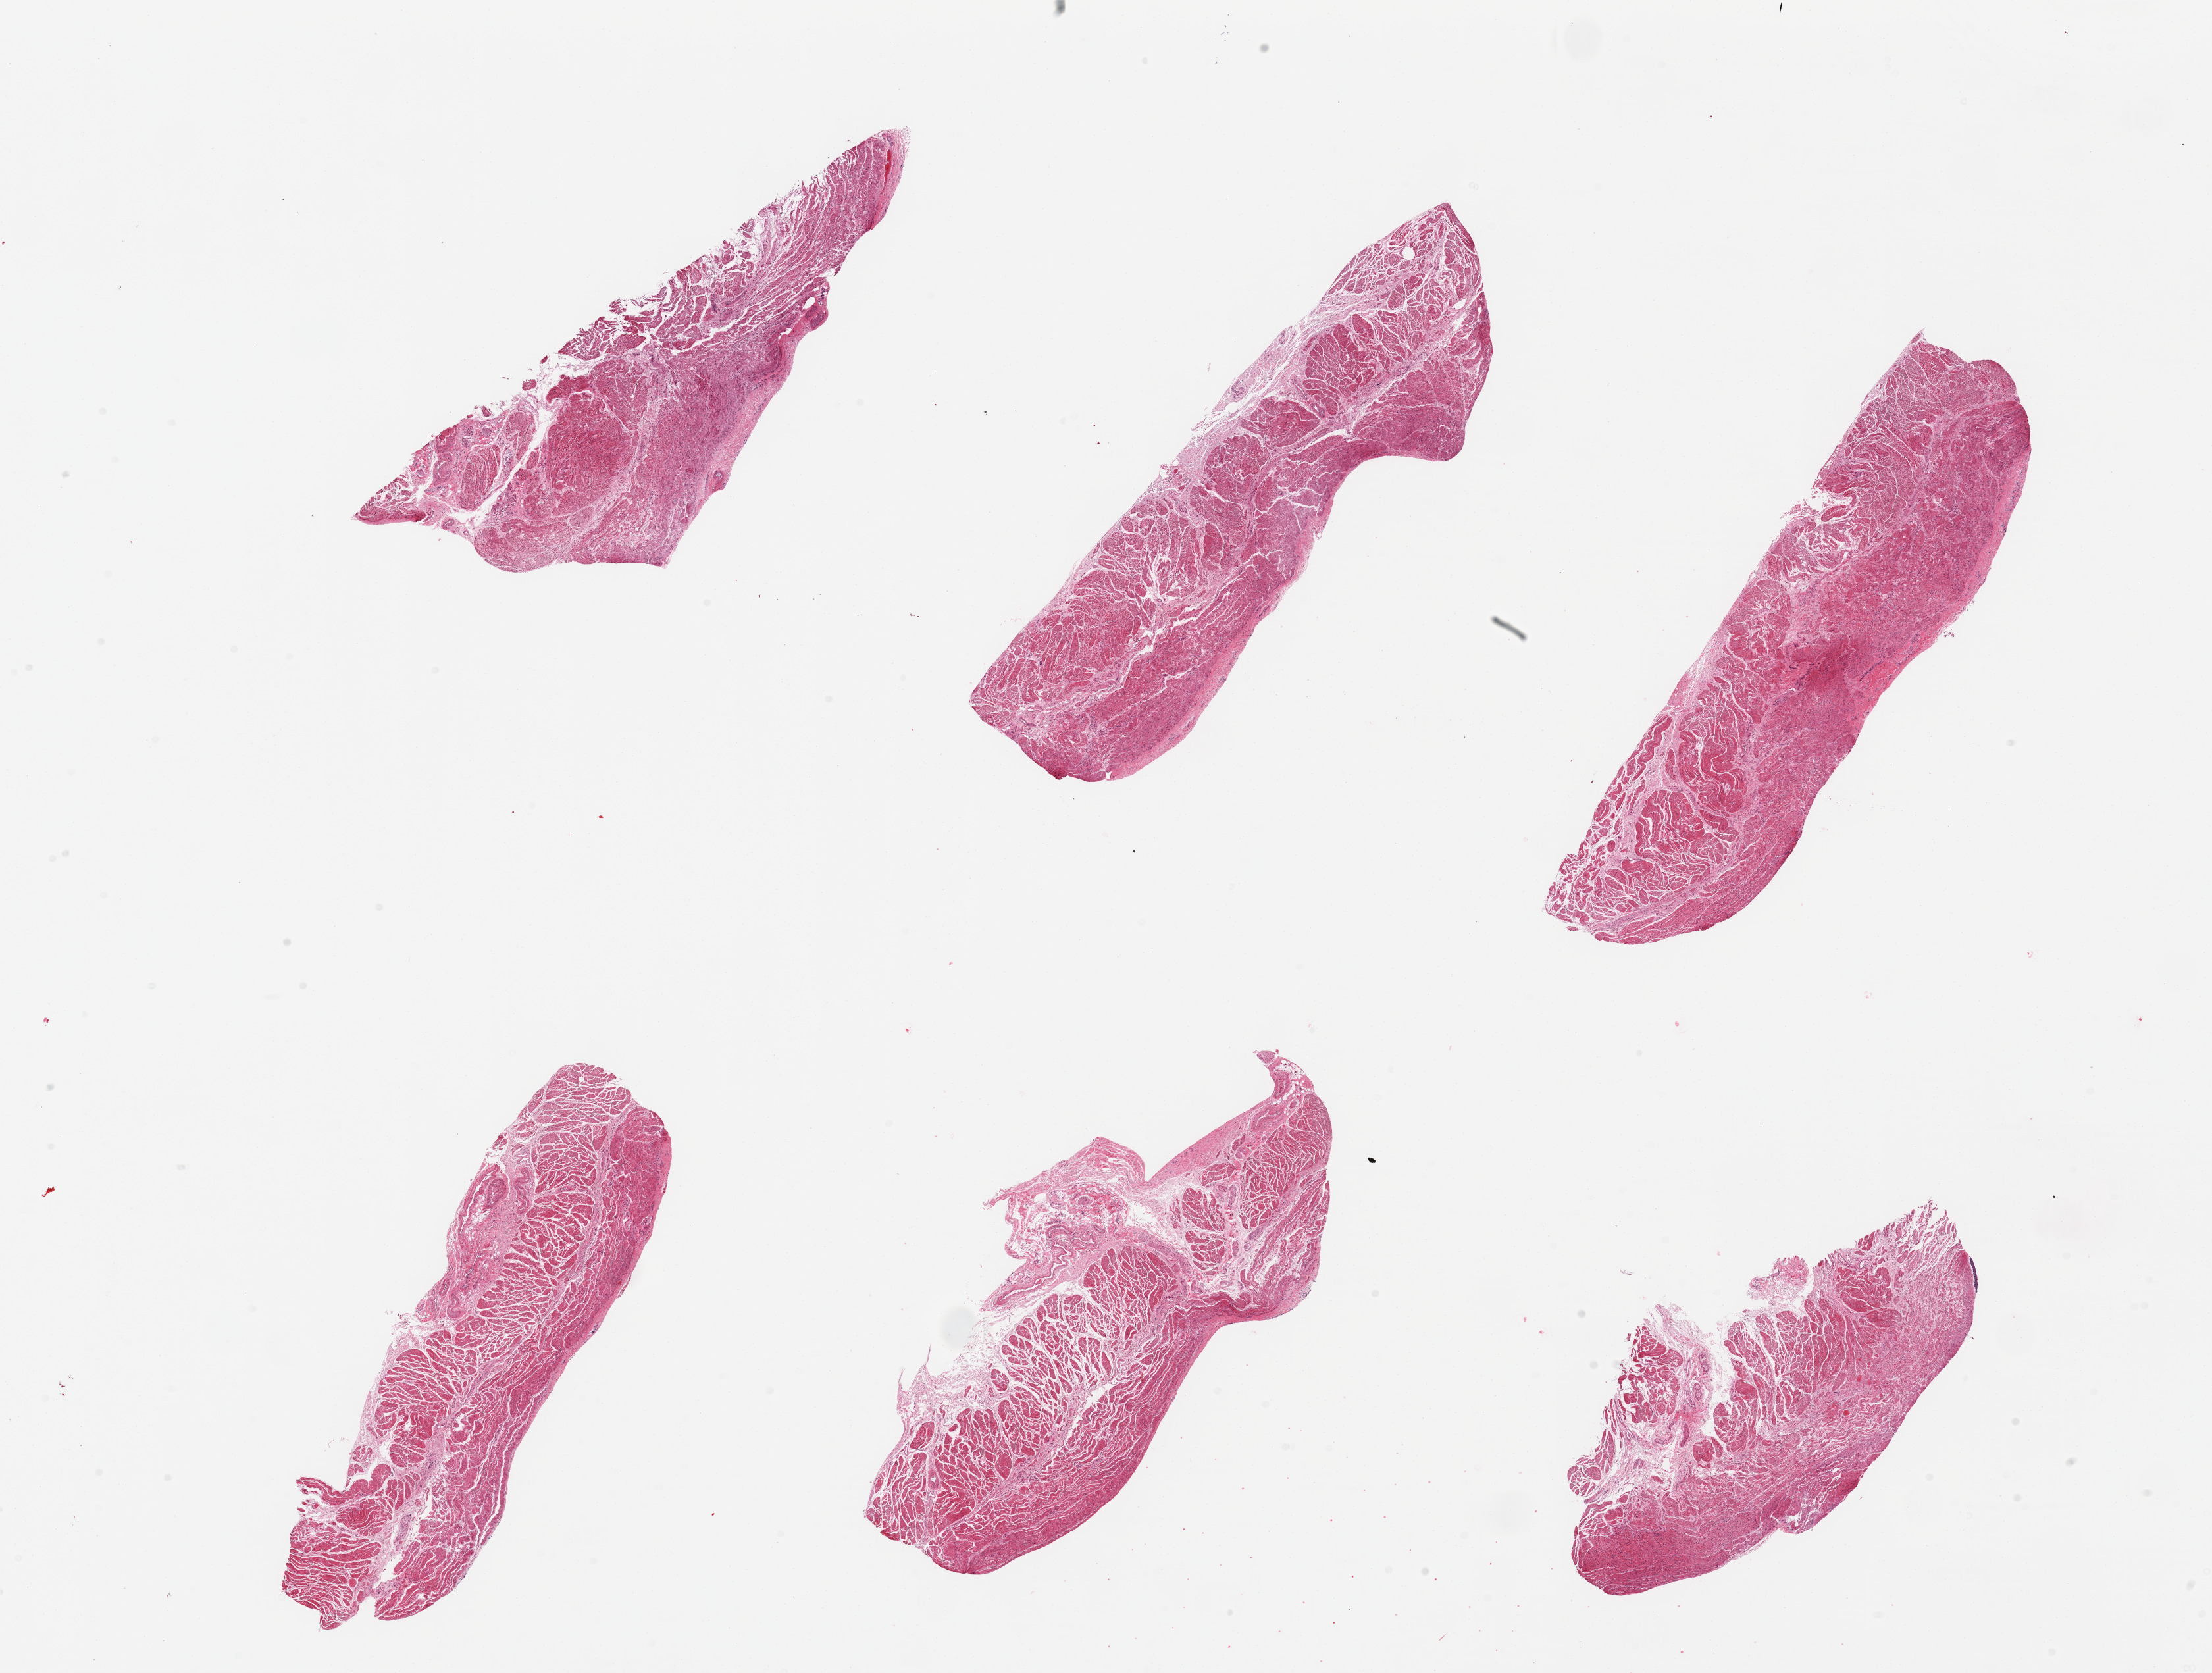
H&E whole-slide image — low-resolution overview of the scanned area, about 26.6 x 20.1 mm; PAXgene-fixed paraffin-embedded (PFPE) section; sampled site (target tissue): gastroesophageal junction; tissue donor sample.
Review note (as recorded): 6 pieces; target muscularis.